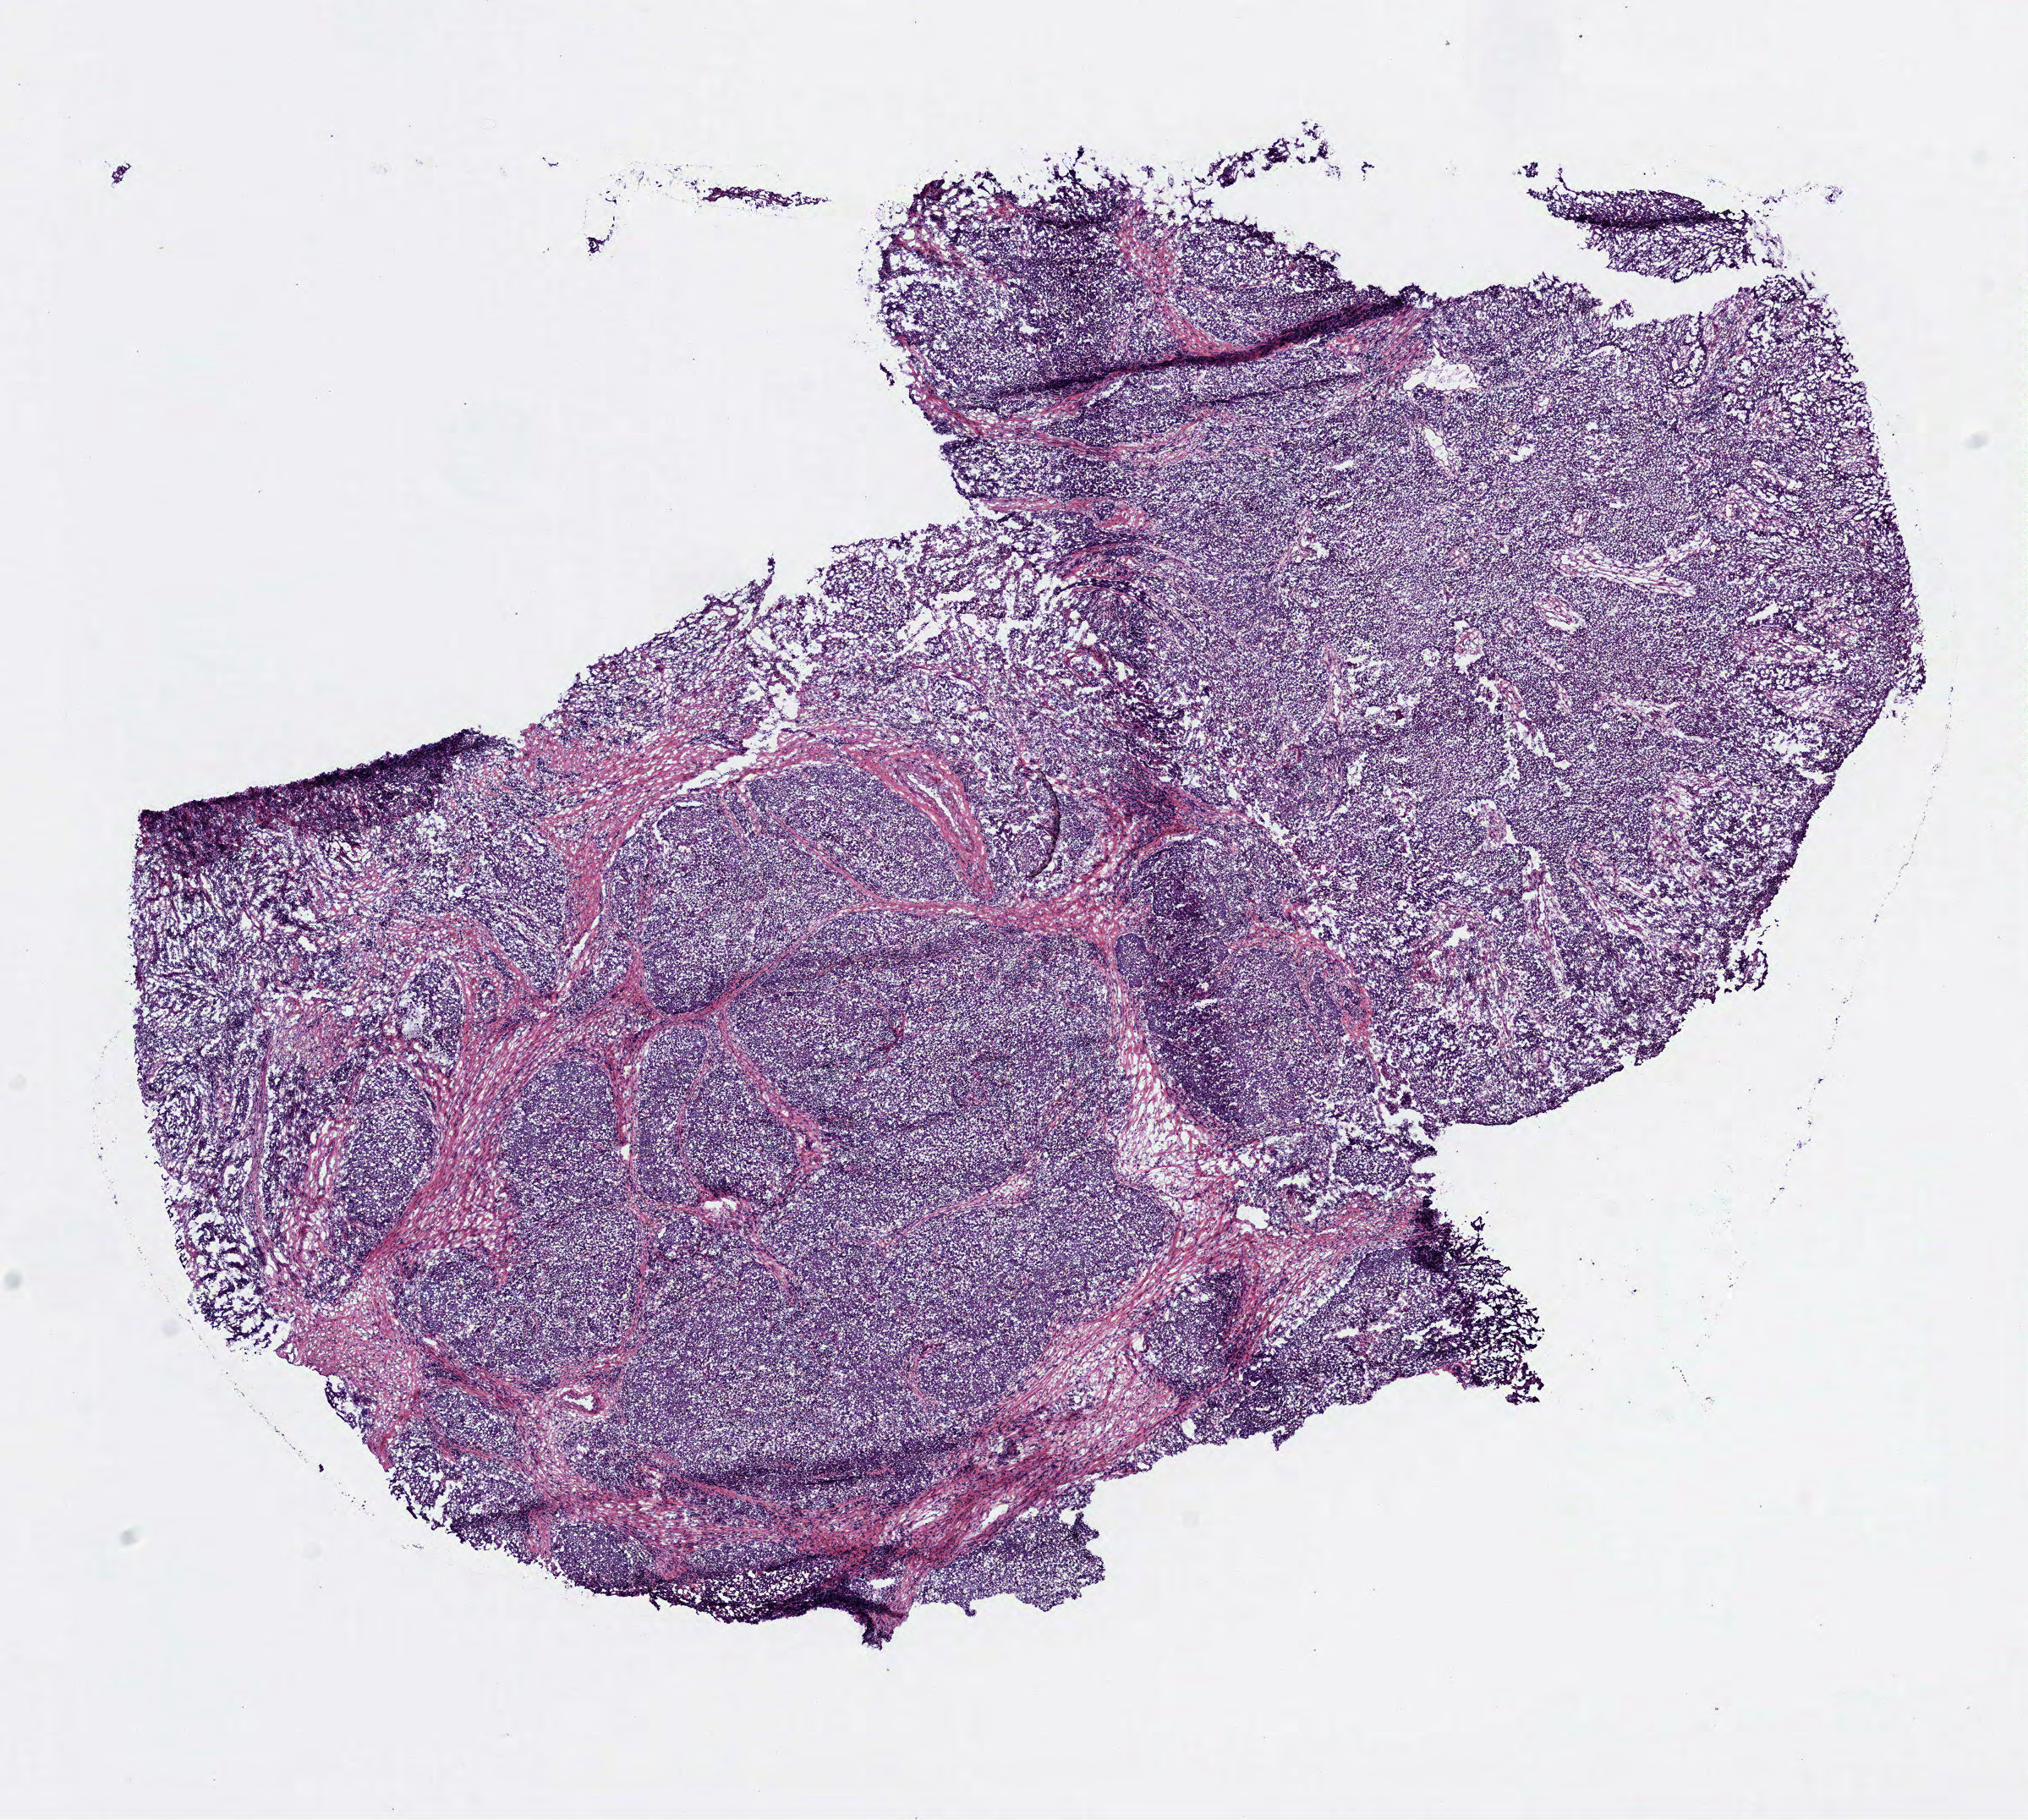
H&E-stained whole-slide image — shown as a low-resolution overview of the whole scanned area (about 9.7 x 8.7 mm). Frozen section. Primary tumour sample from the head and neck. Male patient; age at initial diagnosis 73 years. Histologic grade: GX (grade cannot be assessed). Slide review estimates, as recorded: tumour cells 85%, tumour nuclei 80%, normal cells 0%, stromal cells 10%, necrosis 5%.
AJCC pathologic stage: IVA. Pathologic diagnosis: Squamous cell carcinoma, NOS (larynx, NOS). TNM: T3 N2c M0. Laterality: right.